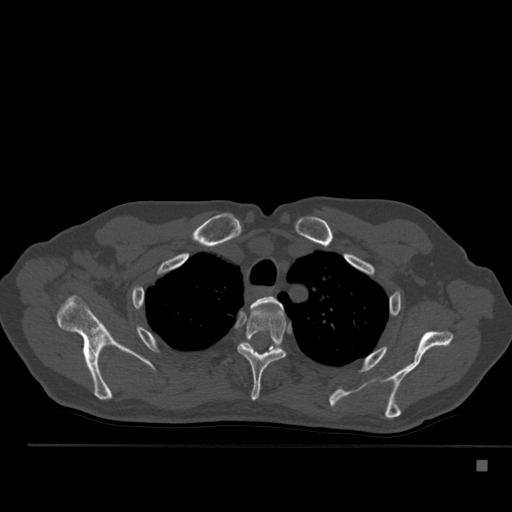
CT including the spine, one axial slice; position 396 of 517 along the scan axis; reconstruction kernel Br40s; bone window (W 1800 / L 400 HU); 1.5 mm slice thickness; 512 × 512 image matrix, field of view 408 × 408 mm. Patient: male, 70 years. Case-level facts recorded for this patient, not image findings: primary cancer: renal.
Structures marked on this image (semi-automatically segmented with operator editing):
- T2 vertebra: bounding box (x1, y1, x2, y2) in pixels: (251, 296, 282, 307)
- T3 vertebra: (237, 307, 286, 401)
- T4 vertebra: (221, 343, 279, 365)